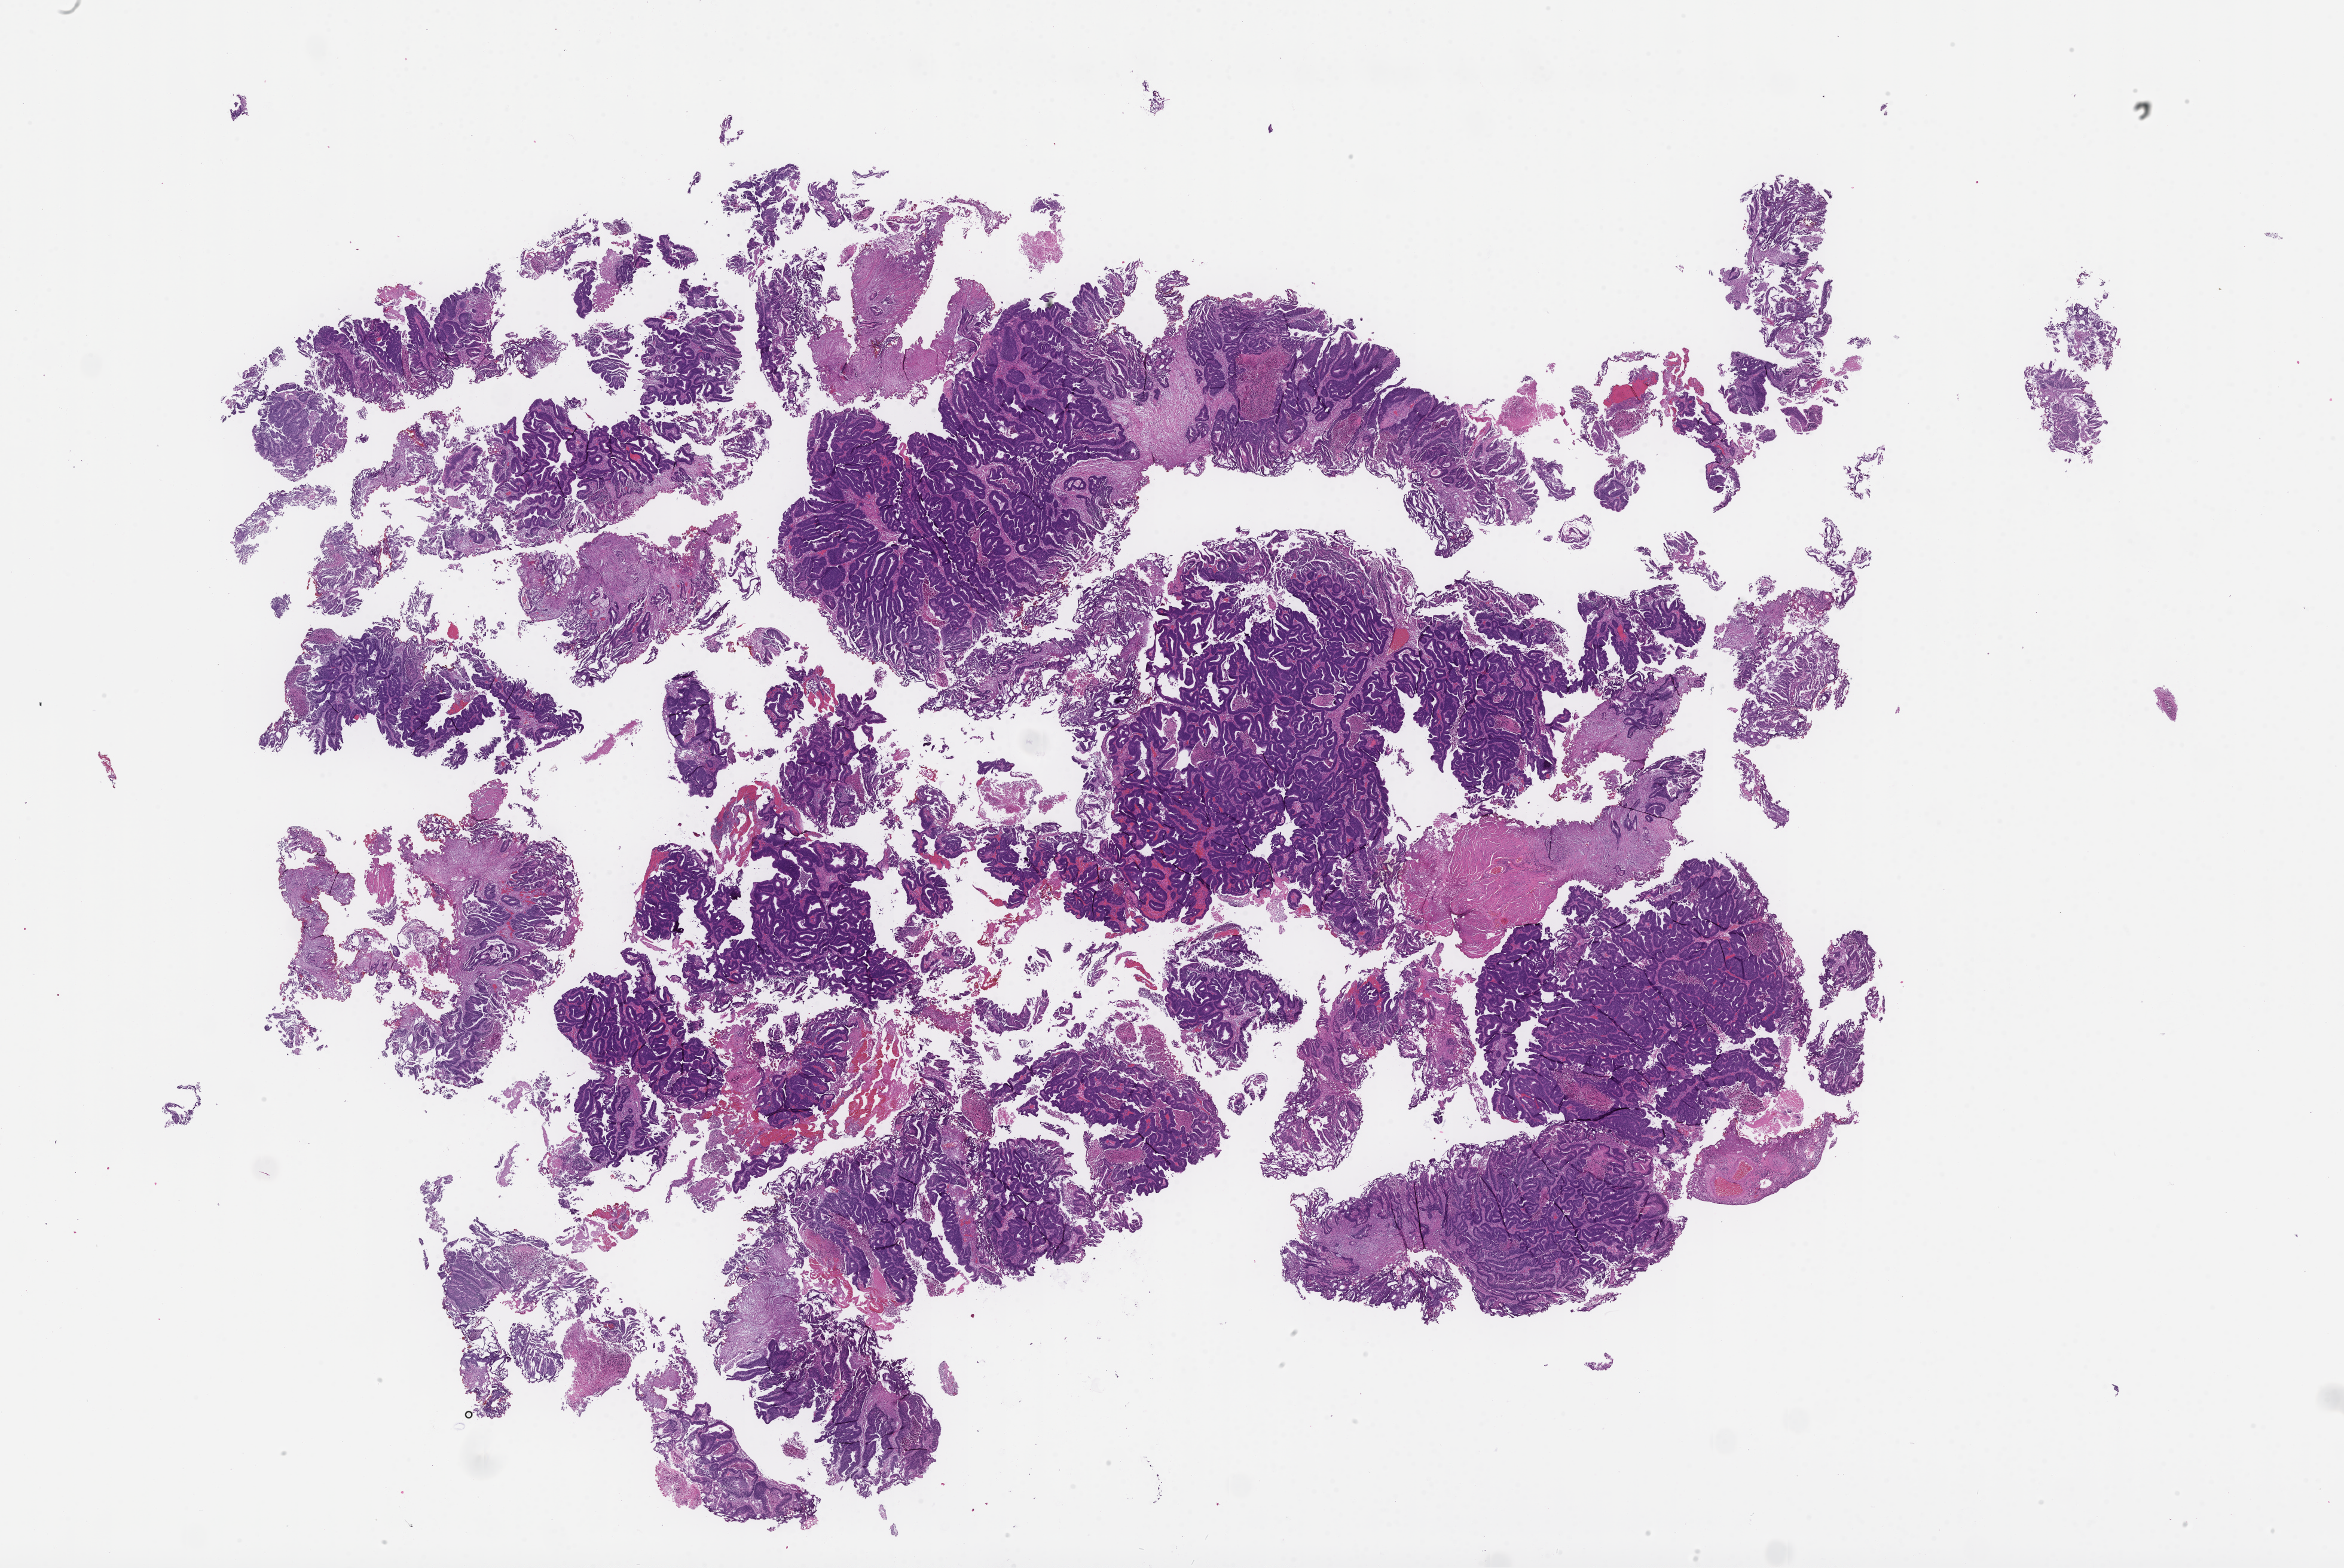
Whole-slide image, haematoxylin and eosin stain, a low-resolution overview of the entire scanned area, about 31.7 x 21.2 mm, FFPE section. Male patient.
This section: metastatic tumor tissue. Primary diagnosis of the patient: Colorectal Carcinoma.